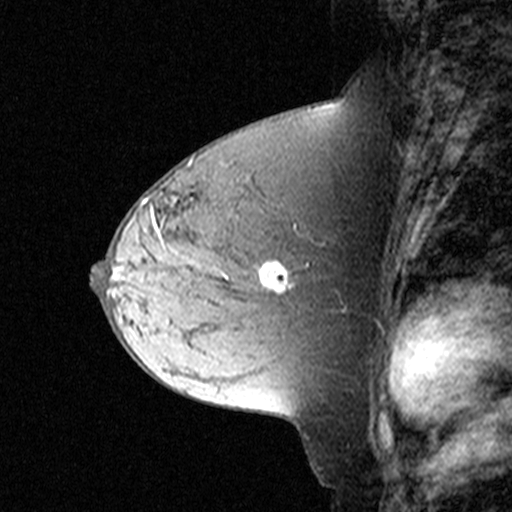
Breast MRI (dynamic contrast-enhanced), one sagittal slice; position 19 of 44 along the scan axis; dynamic contrast-enhanced study with each time point stored as its own series, time point 2 of 3 at this slice position (early post-contrast, ordered by acquisition time); 1.5 T; TE 4.5 ms, TR 11 ms; 512 × 512 image matrix. Patient: female, 44 years. From the clinical record (not read from this slice): setting: breast cancer imaged before/during neoadjuvant chemotherapy; receptor status: triple-negative.
Outlined on this slice (semi-automatic segmentation, software-assisted and operator-edited):
- analysis volume of interest (the breast-tissue region the enhancement analysis was run in; not a lesion): bounding box [x1, y1, x2, y2] px = [174, 204, 303, 305]
- tumour enhancement mask (voxels above the 90 % enhancement threshold inside the analysis volume of interest): [259, 262, 292, 293]